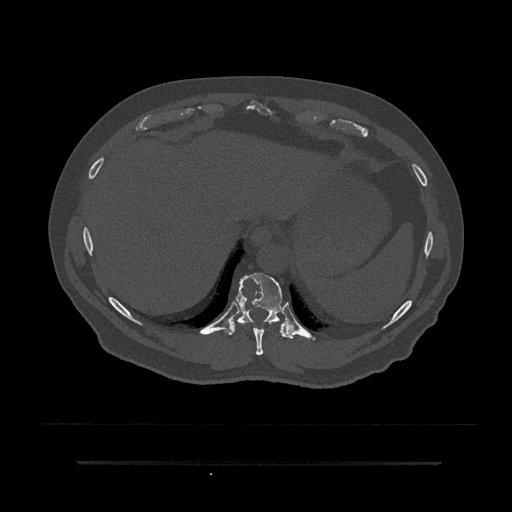
CT including the spine, one axial slice; position 348 of 797 along the scan axis; 120 kVp; bone window (W 1800 / L 400 HU); 0.5 mm slice thickness; 512 × 512 image matrix, field of view 464 × 464 mm. Male patient, age 59 years. From the clinical record (not read from this slice): primary cancer: bile ducts.
Structures marked on this image (semi-automatic segmentation, software-assisted and operator-edited):
- T10 vertebra: box from (x=226, y=273) to (x=294, y=339) px
- T9 vertebra: (x=253, y=327)–(x=264, y=355)